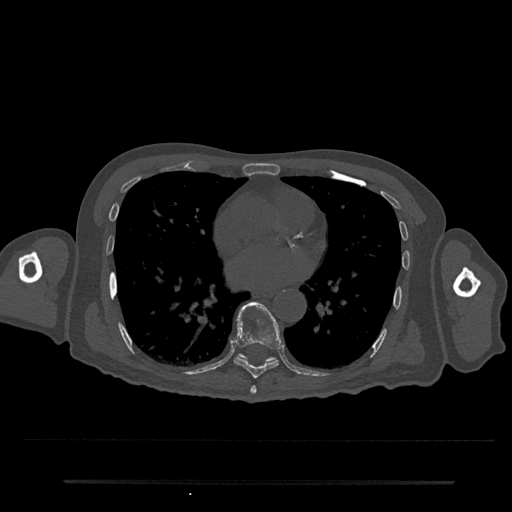
CT including the spine, one axial slice. Position 411 of 797 along the scan axis. 120 kVp. Bone window (W 1800 / L 400 HU). 0.5 mm slice thickness. 512 × 512 image matrix. Patient: male, 74 years. From the clinical record (not read from this slice): primary cancer: prostate.
Outlined on this slice (semi-automatically segmented with operator editing):
- T7 vertebra: bounding box [x1, y1, x2, y2] px = [250, 386, 257, 394]
- T8 vertebra: [234, 302, 281, 379]
- T9 vertebra: [239, 353, 275, 362]